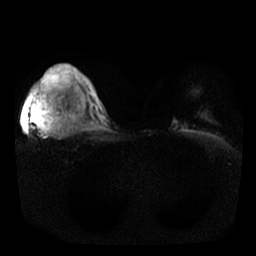
Breast MRI, one axial slice; slice 22 of 25 in the series (ordered by position); diffusion-weighted series; image 2 of 4 stored at this slice position (different b-values; order by instance number); 1.5 T; 4 mm slice thickness; 256 × 256 image matrix, field of view 350 × 350 mm. Female patient.
Structures marked on this image (expert manual segmentation):
- tumour on diffusion-weighted imaging: bounding box (x1, y1, x2, y2) in pixels: (36, 65, 74, 132)